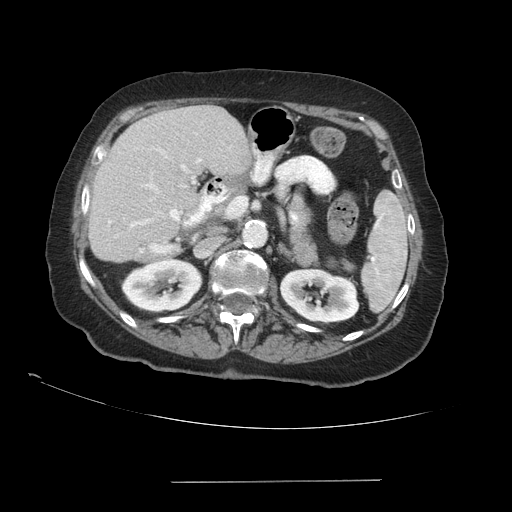
Contrast-enhanced abdominal CT (liver protocol), one axial slice. Slice 50 of 89 in the series (ordered by position). Reconstruction kernel STANDARD. Soft-tissue window (W 400 / L 40 HU). 2.5 mm slice thickness. 512 × 512 image matrix. Case-level facts recorded for this patient, not image findings: diagnosis: hepatocellular carcinoma (patient treated with transarterial chemoembolisation; whether this scan precedes or follows treatment is not stated here); TNM stage (as recorded): Stage-IVA; Child-Pugh class: A; tumour differentiation: poorly differentiated.
Annotated regions visible in this slice (semi-automatic segmentation, software-assisted and operator-edited):
- liver parenchyma outside the tumour (the mass and vessels are separate outlines, so this box may not span the whole liver): bounding box [x1, y1, x2, y2] px = [88, 106, 250, 262]
- liver vessels: [109, 149, 201, 252]